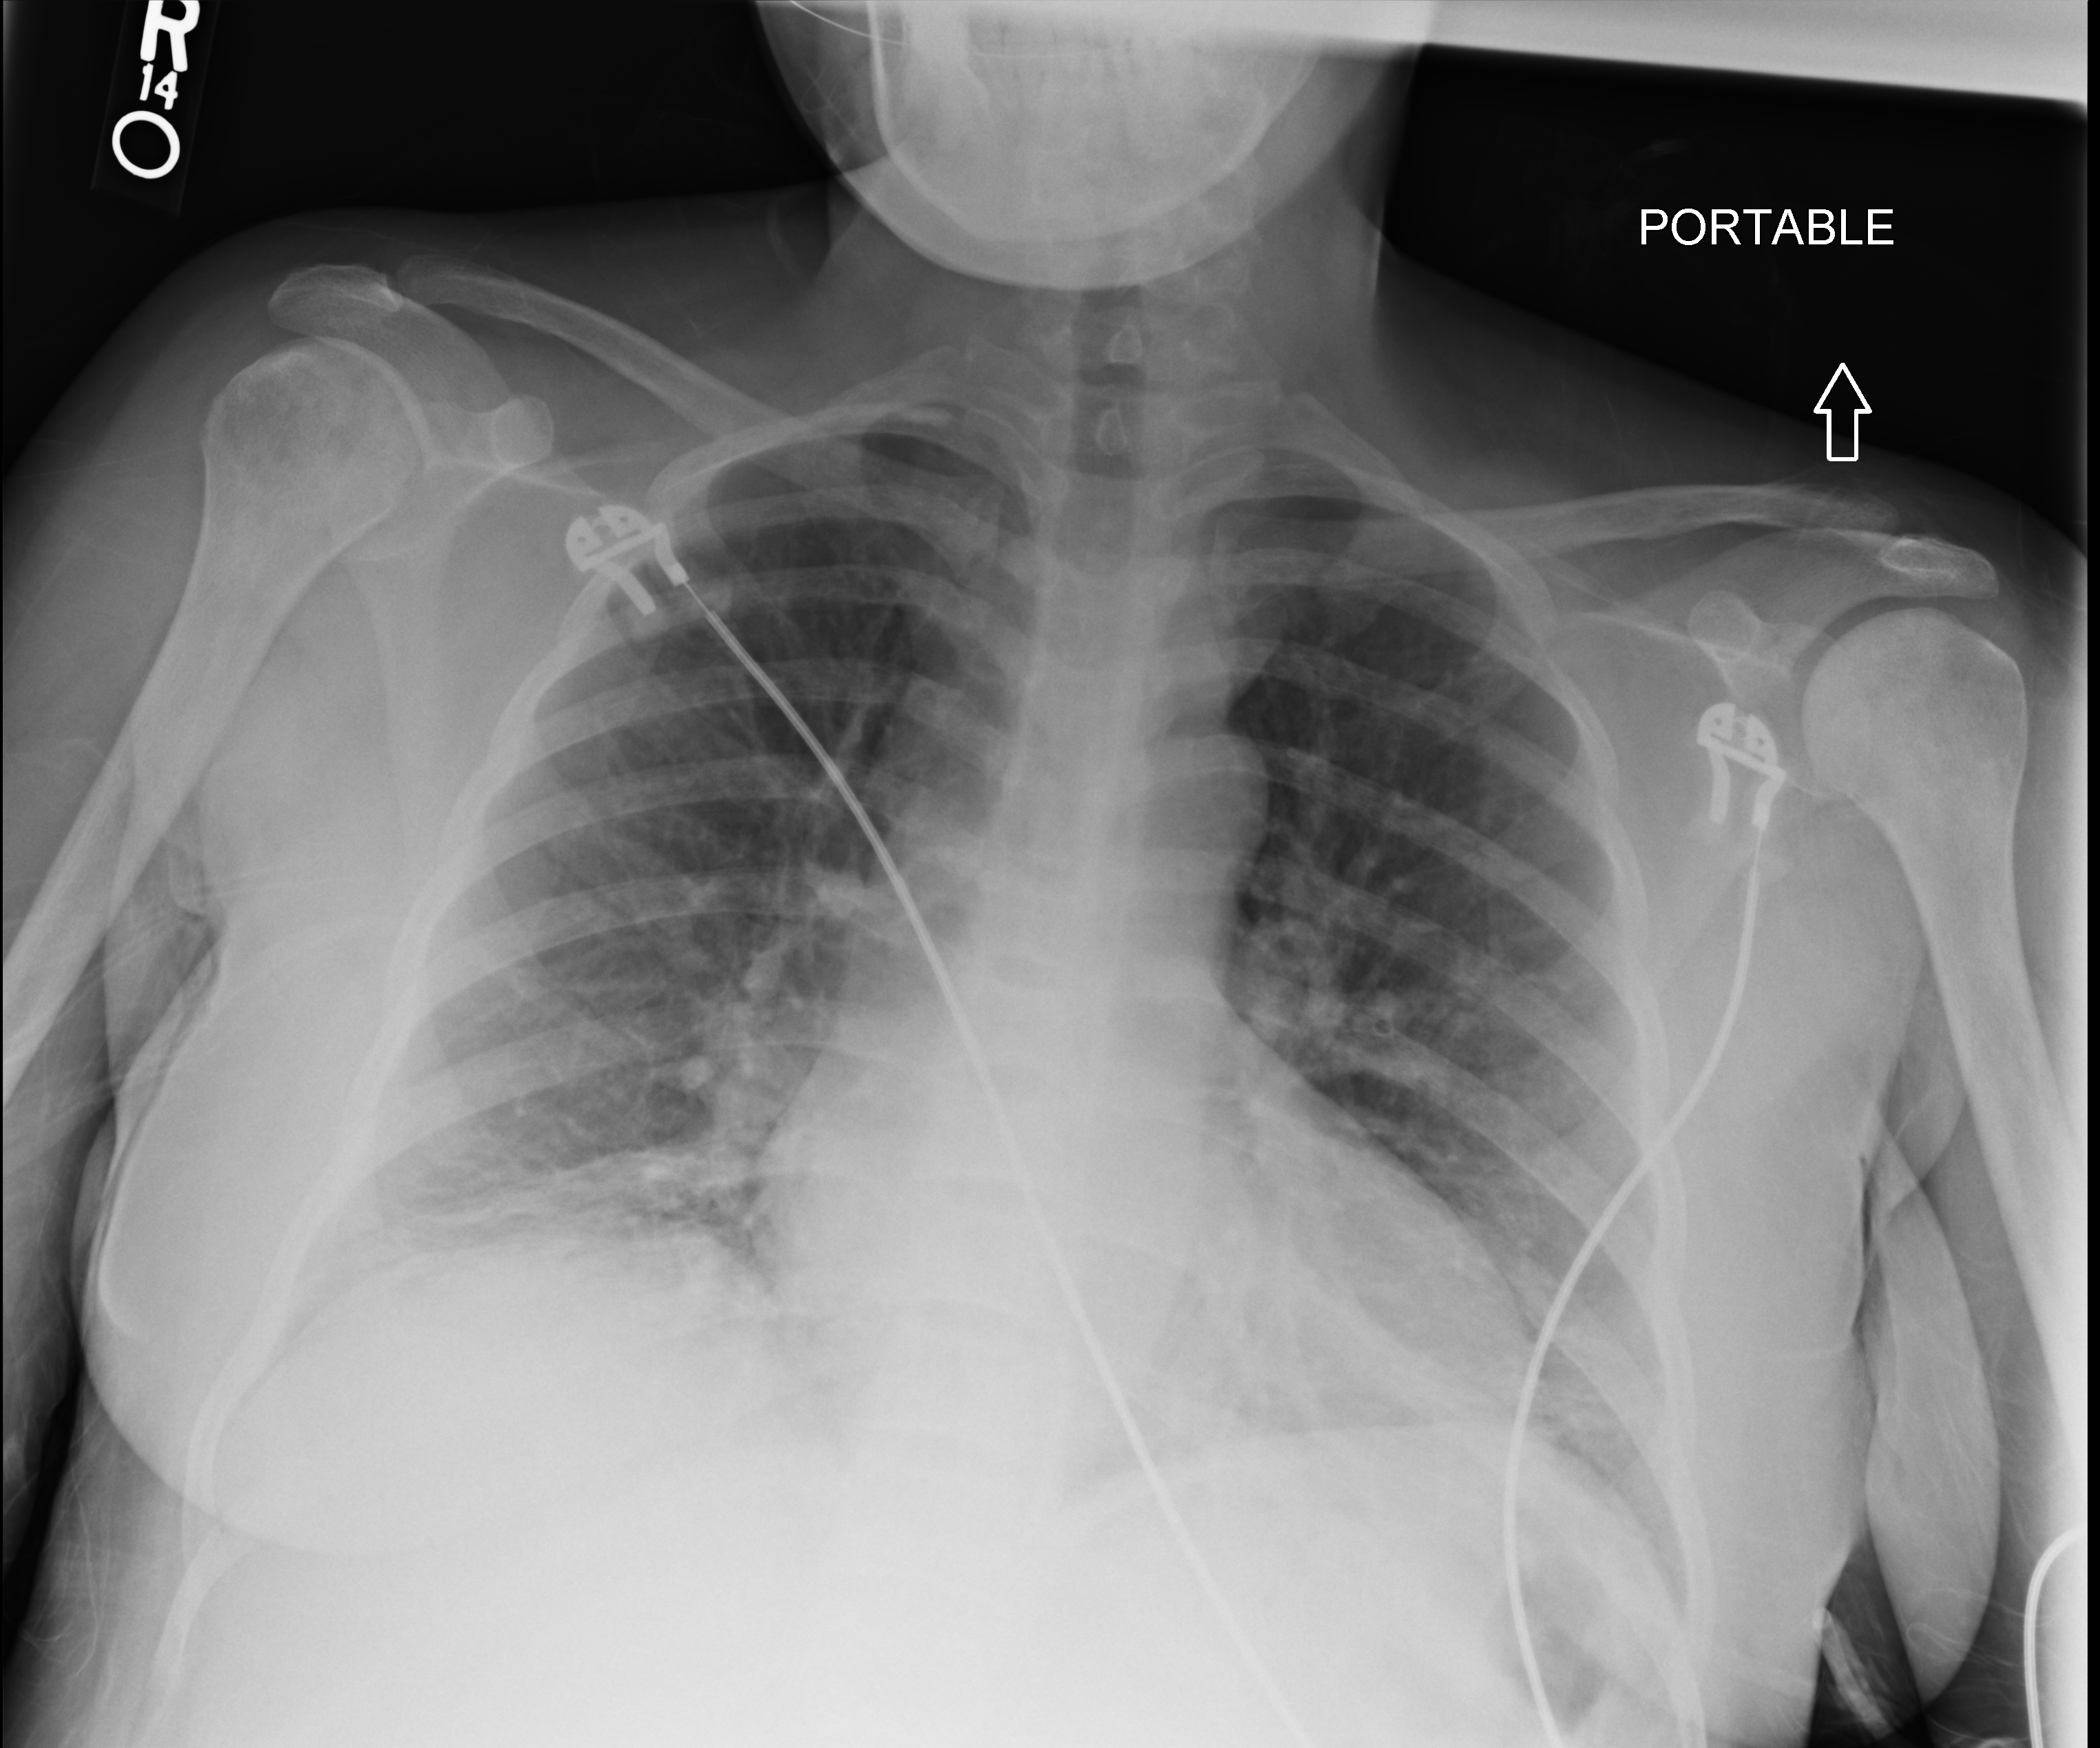
Bedside chest radiograph (computed radiography), anteroposterior (AP) projection. Patient hospitalised with COVID-19; female, aged 18–59 years.
From the hospital-stay record, not from the radiograph (when in the stay this image was taken is not recorded): admitted to intensive care during this hospital stay: no; diabetes (admission record): no.